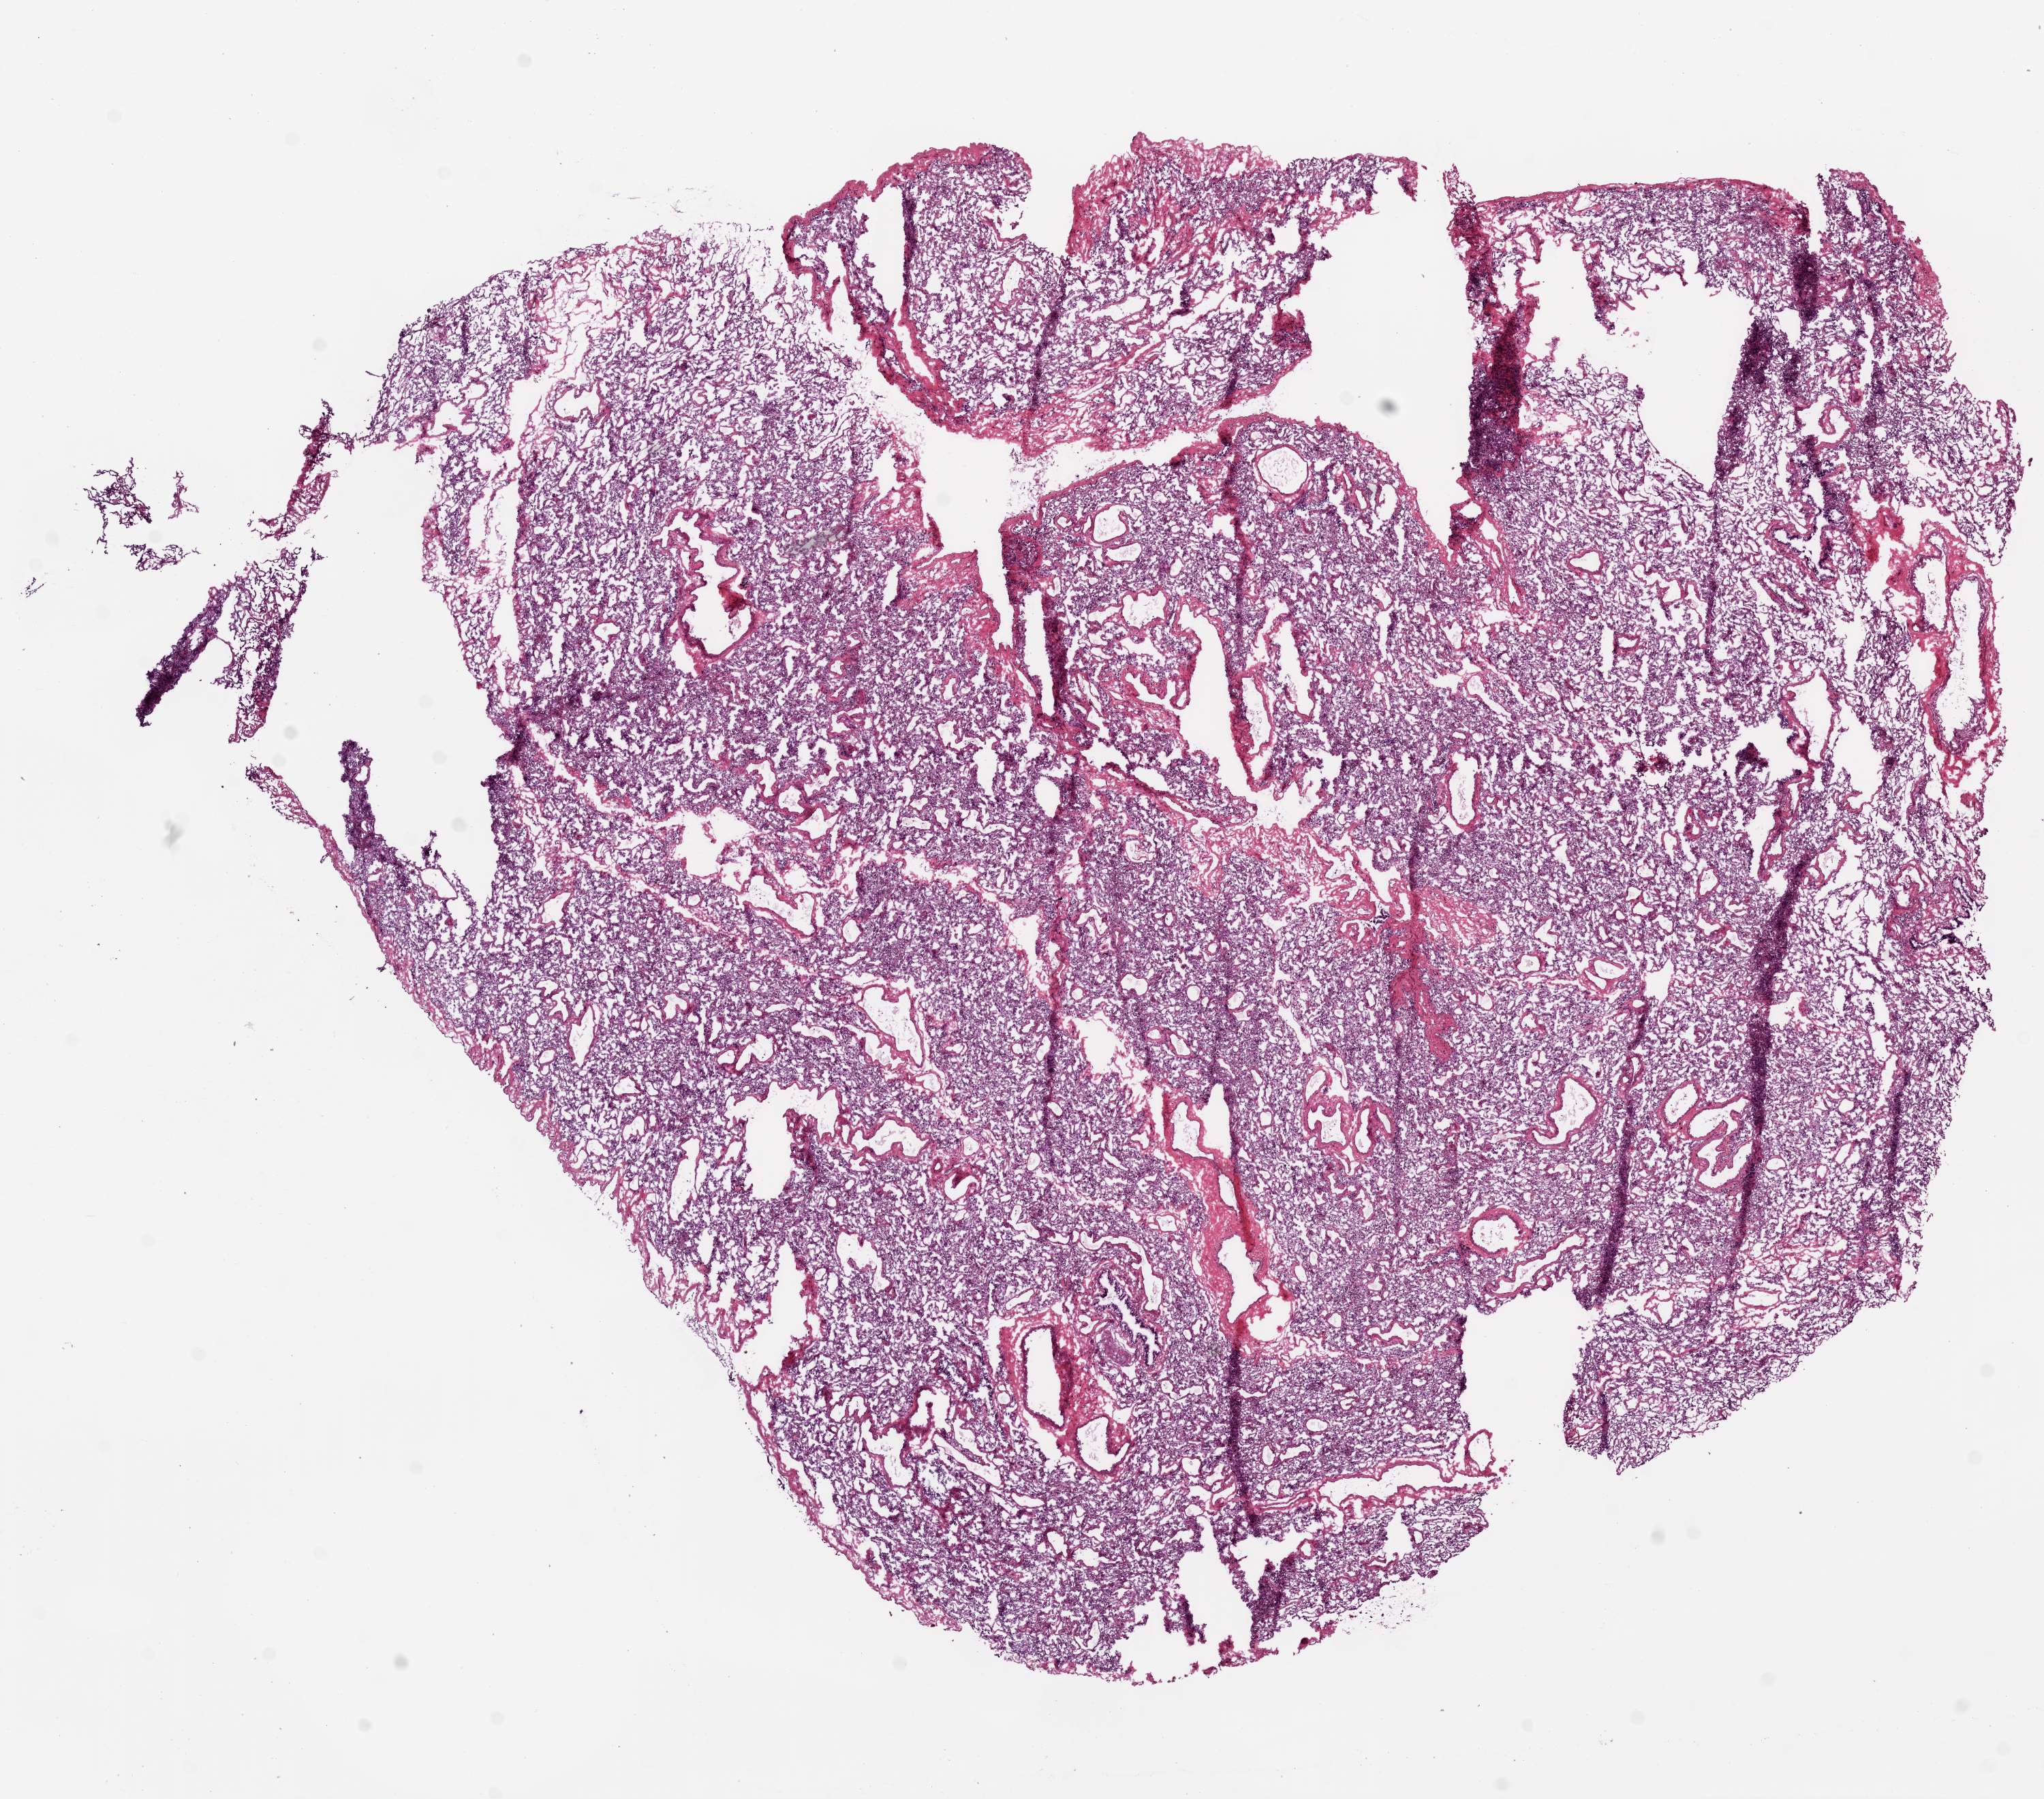
H&E whole-slide image — shown as a low-resolution overview of the whole scanned area (about 12.0 x 10.6 mm, acquisition: 20x scan), frozen section from the bottom of the tissue portion, solid tissue normal (non-tumour tissue) sample from the lung. Female patient; age at initial diagnosis 45 years.
* this section: solid tissue normal (non-tumour) sample from the same patient
* patient diagnosis: Adenocarcinoma, NOS (upper lobe, lung)